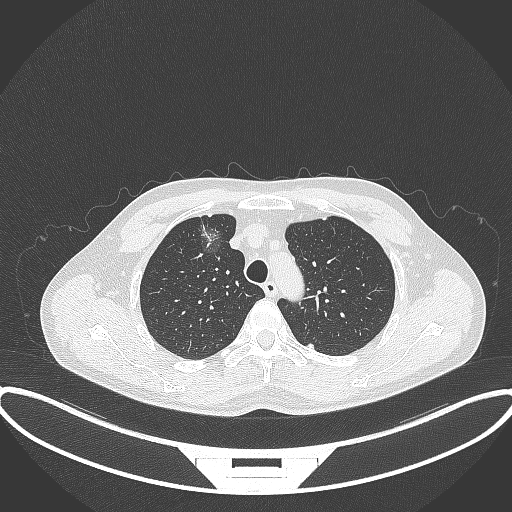
Chest CT, one axial slice; slice 286 of 395 in the series (ordered by position); lung window (W 1500 / L -600 HU); 1 mm slice thickness; 512 × 512 image matrix, field of view 424 × 424 mm. Patient: male, 60 years. From the clinical record (not read from this slice): clinical TNM (as recorded): T1c N0 M0.
Annotated regions visible in this slice (bounding box drawn by a radiologist):
- lung tumour (recorded histology: adenocarcinoma): bounding box [x1, y1, x2, y2] px = [192, 215, 229, 255]